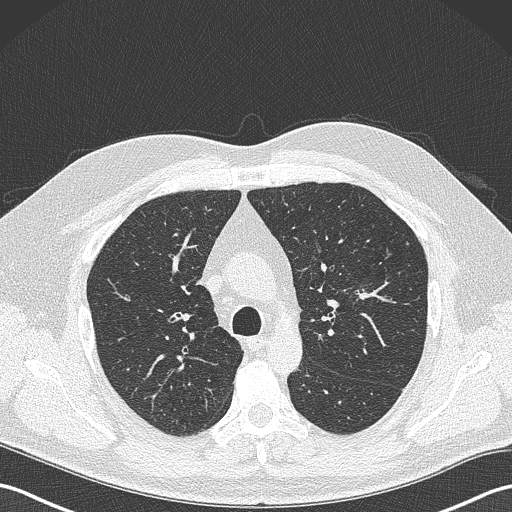
Low-dose screening chest CT, one axial slice. Slice 239 of 343 in the series (ordered by position). 120 kVp. Lung window (W 1500 / L -600 HU). 1 mm slice thickness. 512 × 512 image matrix.
Structures marked on this image (outlined manually by an expert reader):
- lesion 1 (tumor, upper lobe of left lung): bounding box <355,289,370,301> (left, top, right, bottom; pixels)